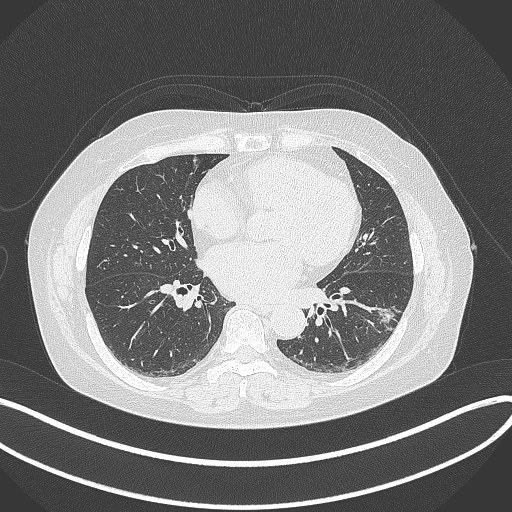
Chest CT, one axial slice. Slice 157 of 373 in the series (ordered by position). Reconstruction kernel B70f. Lung window (W 1500 / L -600 HU). 512 × 512 image matrix, field of view 400 × 400 mm. Patient: female, 67 years. Case-level facts recorded for this patient, not image findings: clinical TNM (as recorded): T1c N0 M0; histopathological grade: G2.
Structures marked on this image (bounding box drawn by a radiologist):
- lung tumour (recorded histology: adenocarcinoma): bounding box <367,298,405,339> (left, top, right, bottom; pixels)